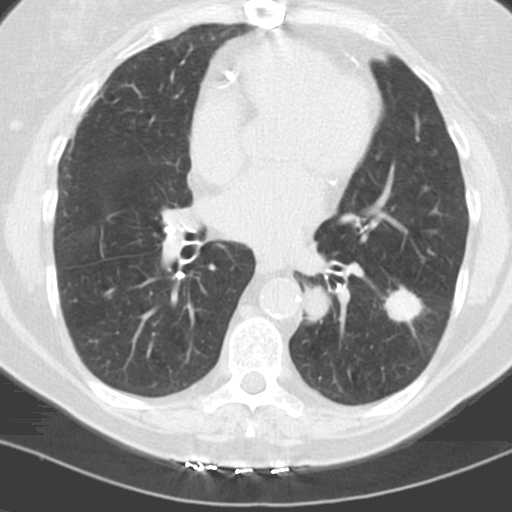
Low-dose screening chest CT, axial slice. Baseline annual screen. Lung window (W 1500 / L -600 HU). Standard (soft-tissue) reconstruction kernel (C). 120 kVp. Slice 70 of 121 in the series. 512 × 512 image matrix, field of view 278 × 278 mm. Female, age 60 years at enrolment.
• 2 expert-annotated lung lesions on this slice (largest first), bounding box <289,280,339,332> (left, top, right, bottom; pixels); <375,286,426,330>.
• The screening reader recorded 3 non-calcified nodules or masses ≥4 mm on this exam (left lower lobe, left lower lobe, right middle lobe); which of them these boxes mark is not recorded.
• Lung cancer was diagnosed 96 days after this screen: adenocarcinoma, NOS, left lower lobe, stage IV (AJCC 6th edition), 22 mm at pathology.